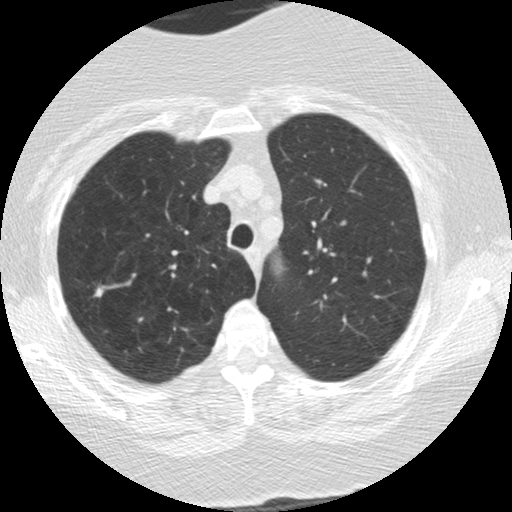
Low-dose screening chest CT, one axial slice; slice 134 of 166 in the series (ordered by position); reconstruction kernel STANDARD; 120 kVp; lung window (W 1500 / L -600 HU); 2.5 mm slice thickness; 512 × 512 image matrix, field of view 309 × 309 mm.
Outlined on this slice (manually delineated by an expert):
- lesion 2 (tumor, upper lobe of right lung): bounding box (x1, y1, x2, y2) in pixels: (94, 286, 104, 297)